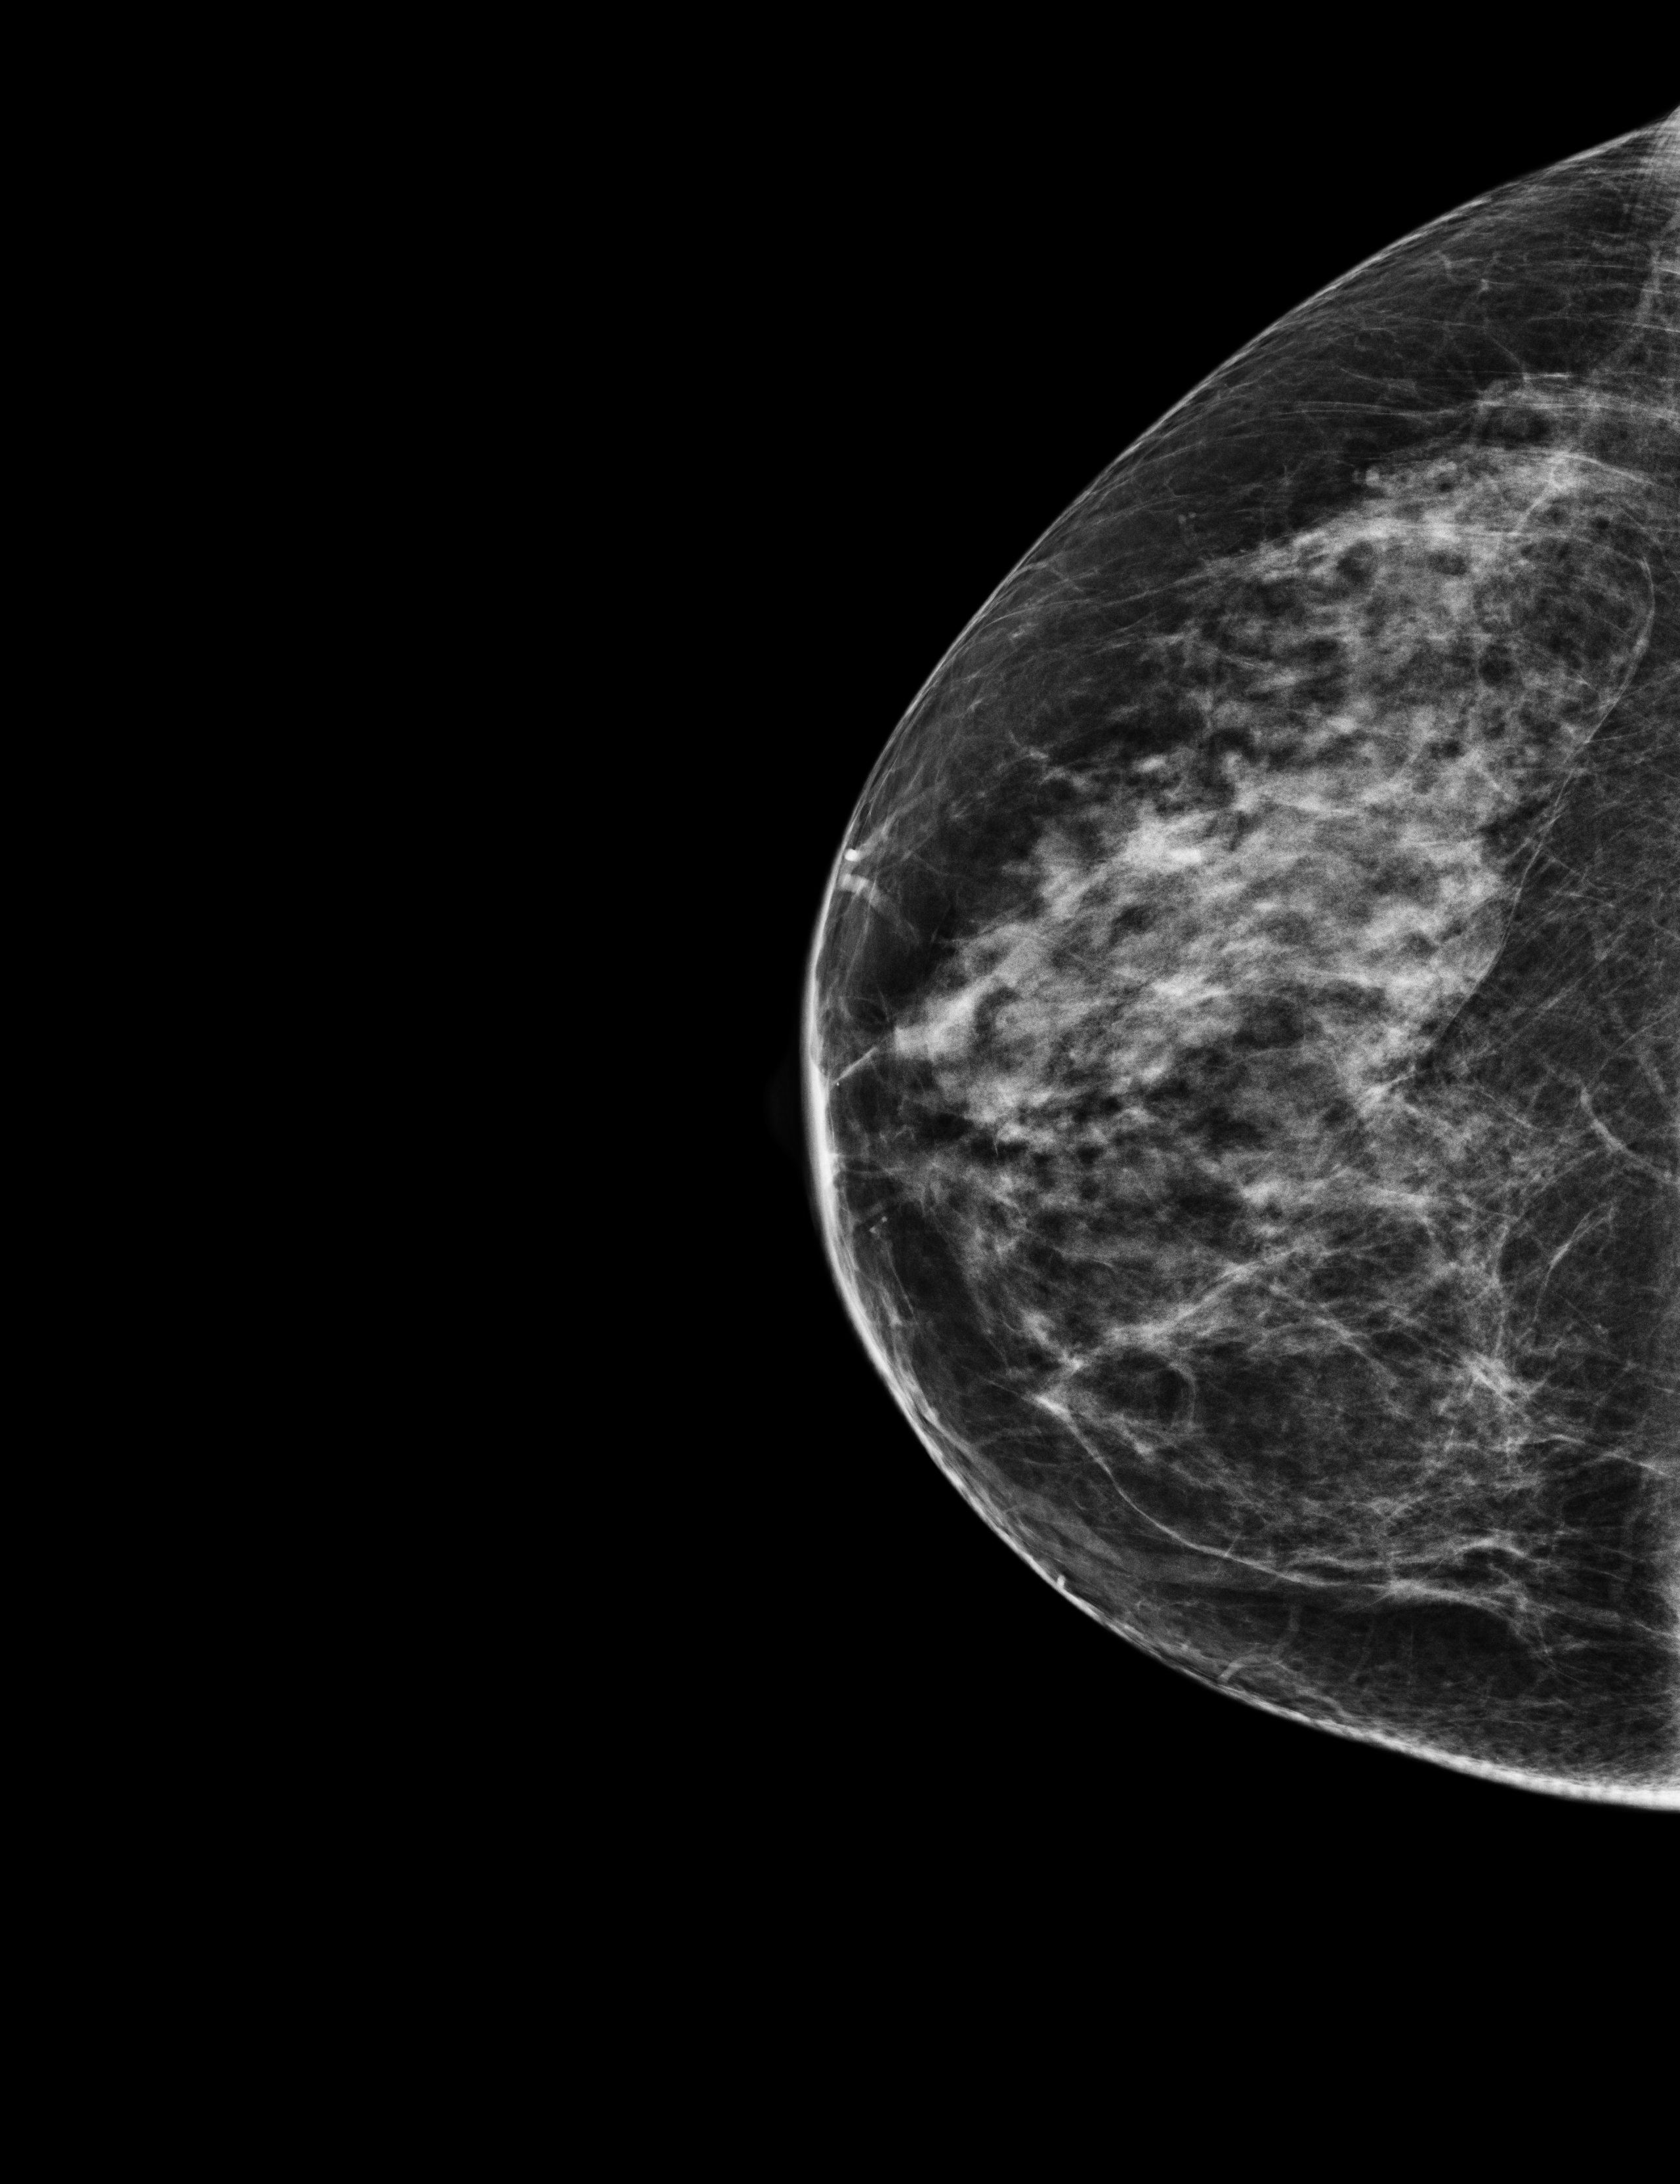
Full-field digital mammogram (FFDM), right breast, CC view, screening examination. Patient: female, 56 years.
Breast density at the screening exam (both breasts): heterogeneously dense (BI-RADS density category c). Final BI-RADS category for the screening round (tomosynthesis exam, both breasts): category 1. Recall: no recall after this screen.